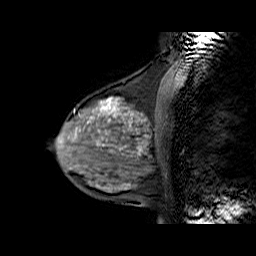
Breast MRI (dynamic contrast-enhanced), one sagittal slice; dynamic contrast-enhanced series, time point 2 of 6 at this slice position (early post-contrast); 1.5 T; TE 6.3 ms, TR 32.9 ms; 4 mm slice thickness; 256 × 256 image matrix, field of view 200 × 200 mm. Female patient. From the clinical record (not read from this slice): setting: breast cancer imaged before/during neoadjuvant chemotherapy; receptor status: HR-positive, HER2-negative.
Structures marked on this image (semi-automatic segmentation, software-assisted and operator-edited):
- analysis volume of interest (the breast-tissue region the enhancement analysis was run in; not a lesion): bounding box [x1, y1, x2, y2] px = [57, 86, 169, 170]
- tumour enhancement mask (voxels above the 100 % enhancement threshold inside the analysis volume of interest): [87, 97, 146, 124]